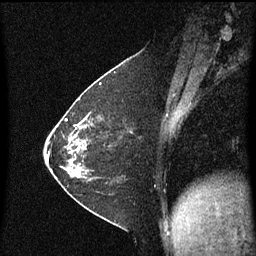
Breast MRI (dynamic contrast-enhanced), one sagittal slice; position 25 of 60 along the scan axis; dynamic contrast-enhanced series, image 2 of 3 at this slice position (ordered by acquisition); 1.5 T; TE 4.2 ms, TR 8.4 ms; 2 mm slice thickness; 256 × 256 image matrix. Female patient, age 36 years. Case-level facts recorded for this patient, not image findings: setting: breast cancer imaged before/during neoadjuvant chemotherapy; receptor status: HR-positive, HER2-negative.
Outlined on this slice (semi-automatic segmentation, software-assisted and operator-edited):
- analysis volume of interest (the breast-tissue region the enhancement analysis was run in; not a lesion): bounding box [x1, y1, x2, y2] px = [72, 116, 123, 181]
- tumour enhancement mask (voxels above the 70 % enhancement threshold inside the analysis volume of interest): [72, 118, 87, 171]